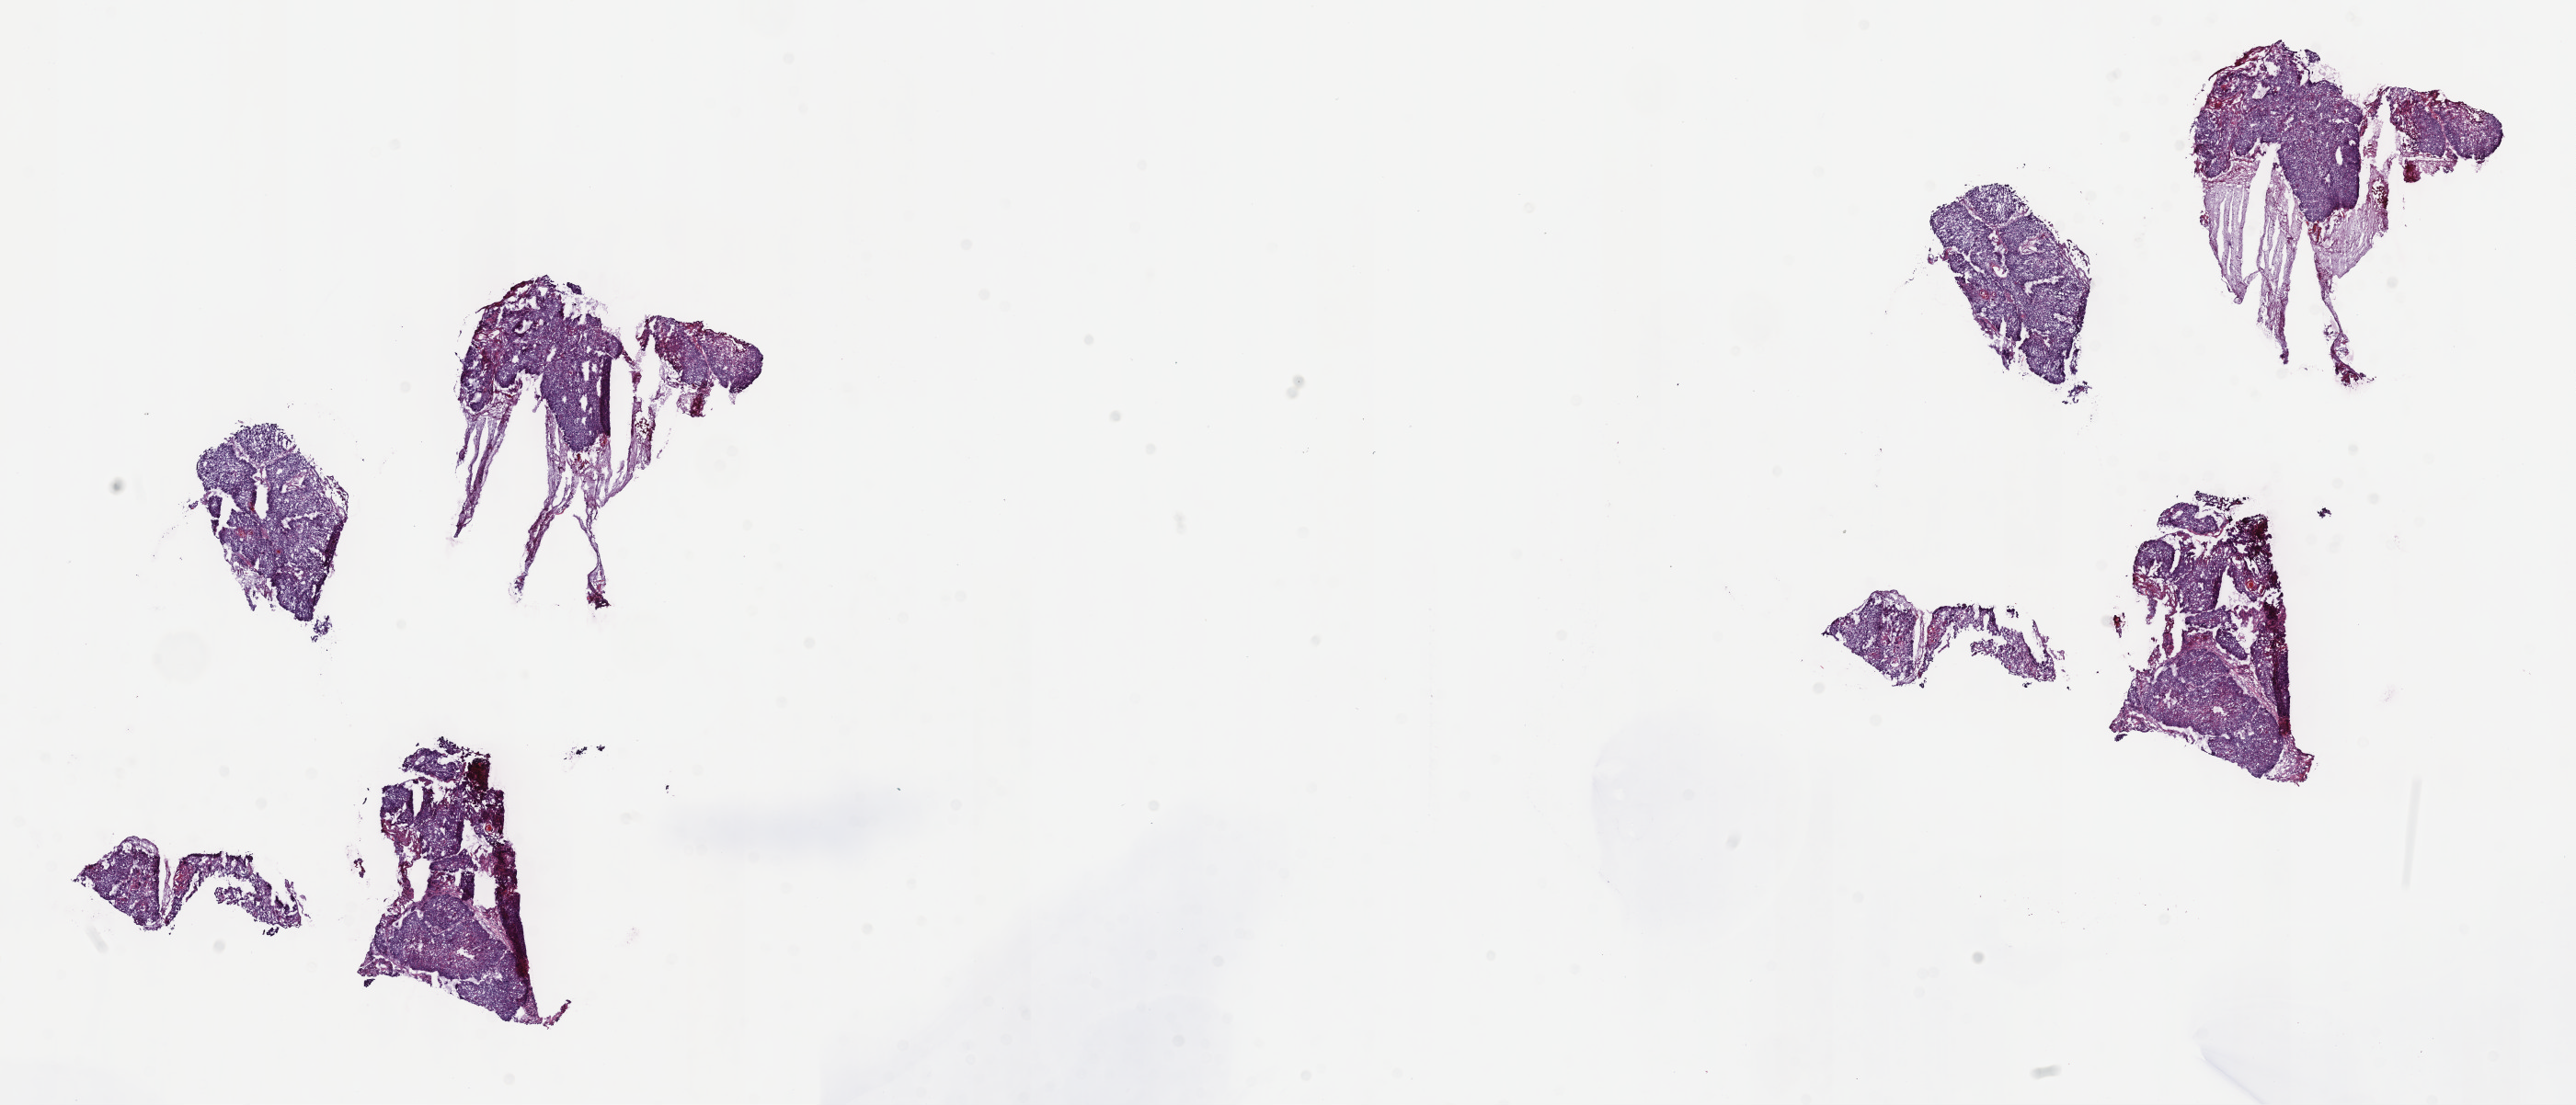
Whole-slide histology image, H&E-stained, low-resolution overview of the scanned area, about 22.7 x 9.7 mm, frozen section from the top of the tissue portion, primary tumour sample from the head and neck. Patient: male, age at initial diagnosis 60 years. Histologic grade: G2 (moderately differentiated). Slide review estimates, as recorded: tumour cells 75%, tumour nuclei 75%, normal cells 0%, stromal cells 25%, necrosis 0%. Inflammatory infiltration, as recorded: lymphocyte infiltration 5%, monocyte infiltration 0%, neutrophil infiltration 0%.
• pathologic diagnosis: Squamous cell carcinoma, NOS (oropharynx, NOS)
• laterality: right